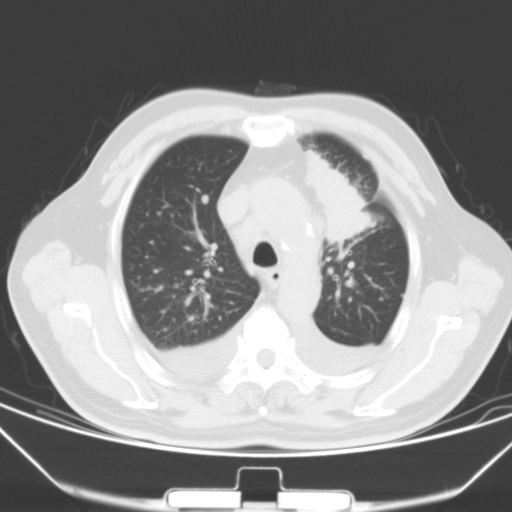
Chest CT, one axial slice. Position 47 of 66 along the scan axis. 120 kVp. Lung window (W 1500 / L -600 HU). 5 mm slice thickness. 512 × 512 image matrix, field of view 352 × 352 mm. Male patient, age 66 years. From the clinical record (not read from this slice): clinical TNM (as recorded): T1c N0 M0.
Structures marked on this image (bounding box drawn by a radiologist):
- lung tumour (recorded histology: adenocarcinoma): bounding box [x1, y1, x2, y2] px = [298, 148, 371, 244]